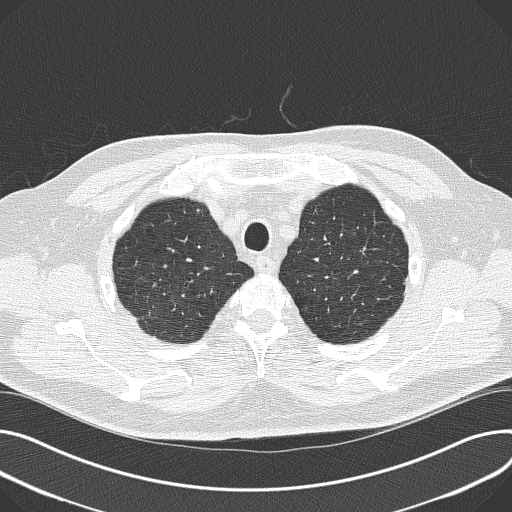
Axial slice from a low-dose chest CT screening exam; third annual screen; lung window (W 1500 / L -600 HU); 2 mm slice thickness; 512 × 512 image matrix, field of view 376 × 376 mm. Male participant, aged 68 years at enrolment.
Expert reader's lesion annotation, bounding box (x1, y1, x2, y2) in pixels: (179, 196, 213, 226). The screening reader recorded 3 non-calcified nodules or masses ≥4 mm on this exam (right upper lobe, left lower lobe, right lower lobe); which of them this box marks is not recorded. Official screen result: positive, other. Lung cancer was diagnosed 95 days after this screen: combined small cell carcinoma, right upper lobe, undifferentiated (G4), stage IIIB (AJCC 6th edition), 30 mm at pathology.